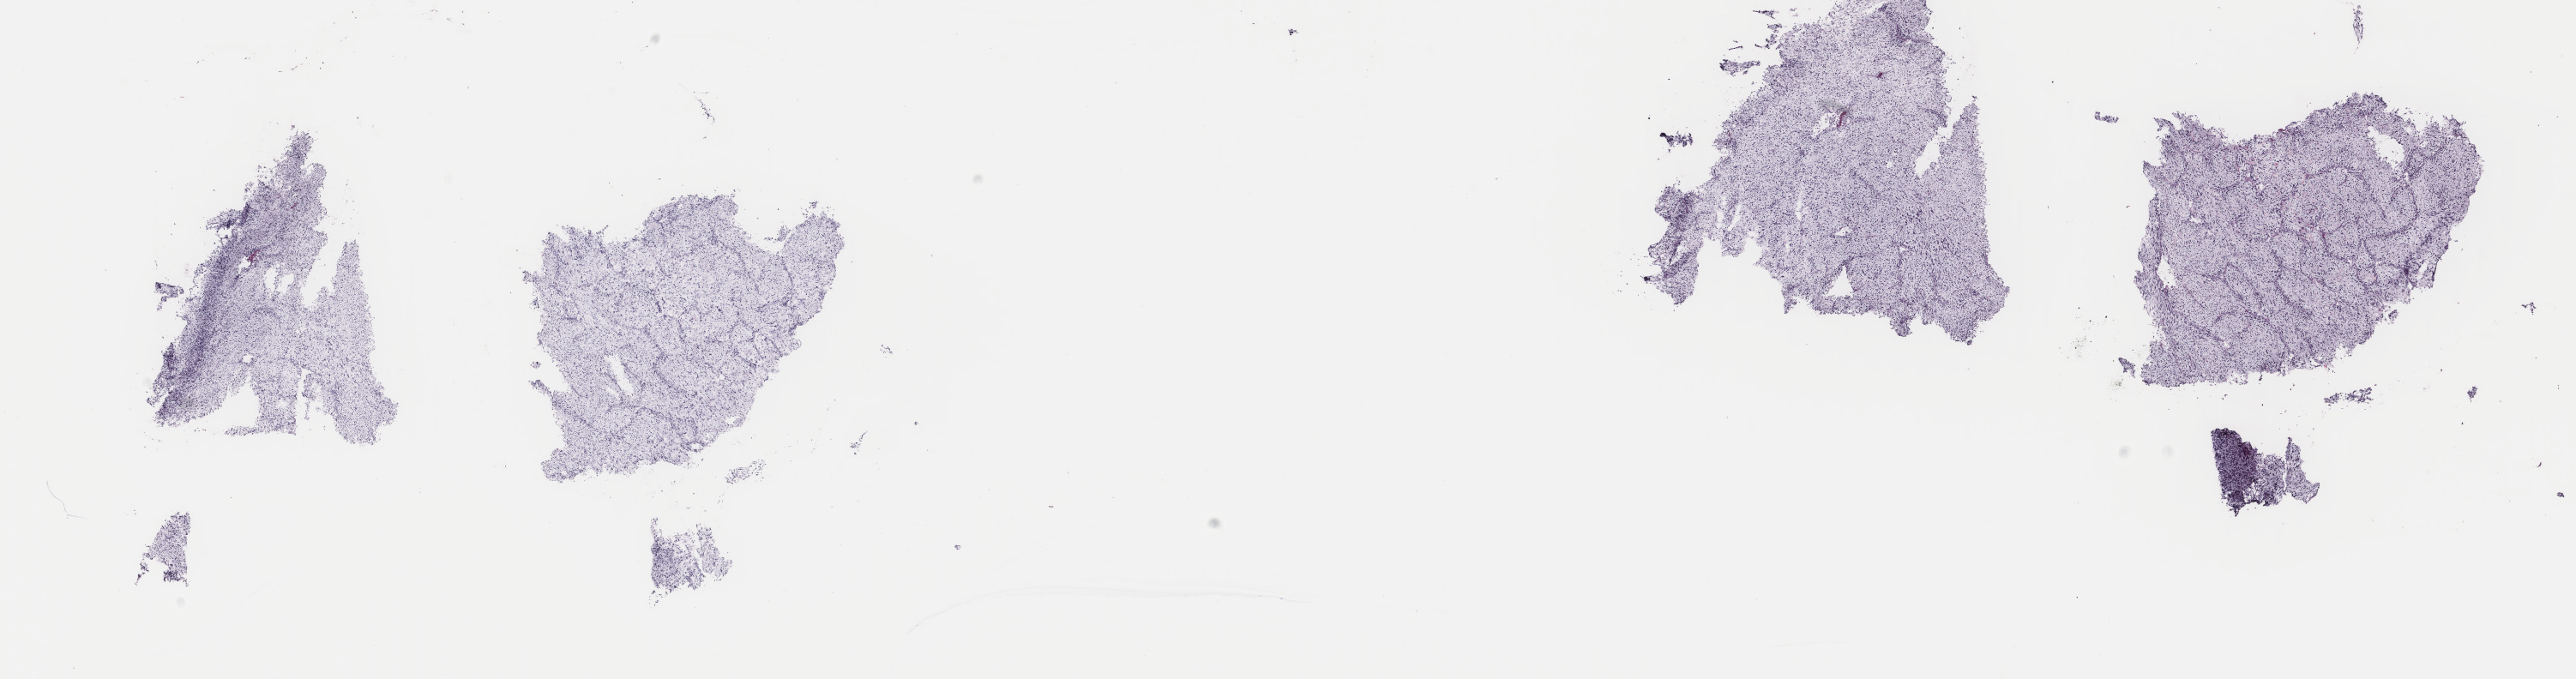
Digitized H&E tissue section (whole slide) — shown as a low-resolution overview of the whole scanned area (about 23.8 x 6.3 mm, acquisition: 40x scan). Frozen section from the top of the tissue portion. Sample: primary tumour, kidney. Male patient; age at initial diagnosis 75 years. Slide review estimates, as recorded: tumour cells 100%, tumour nuclei 95%, normal cells 0%, stromal cells 0%, necrosis 0%. Infiltration values recorded for this section: lymphocyte infiltration 0%, monocyte infiltration 0%, neutrophil infiltration 0%.
Histologic diagnosis: Giant cell sarcoma.